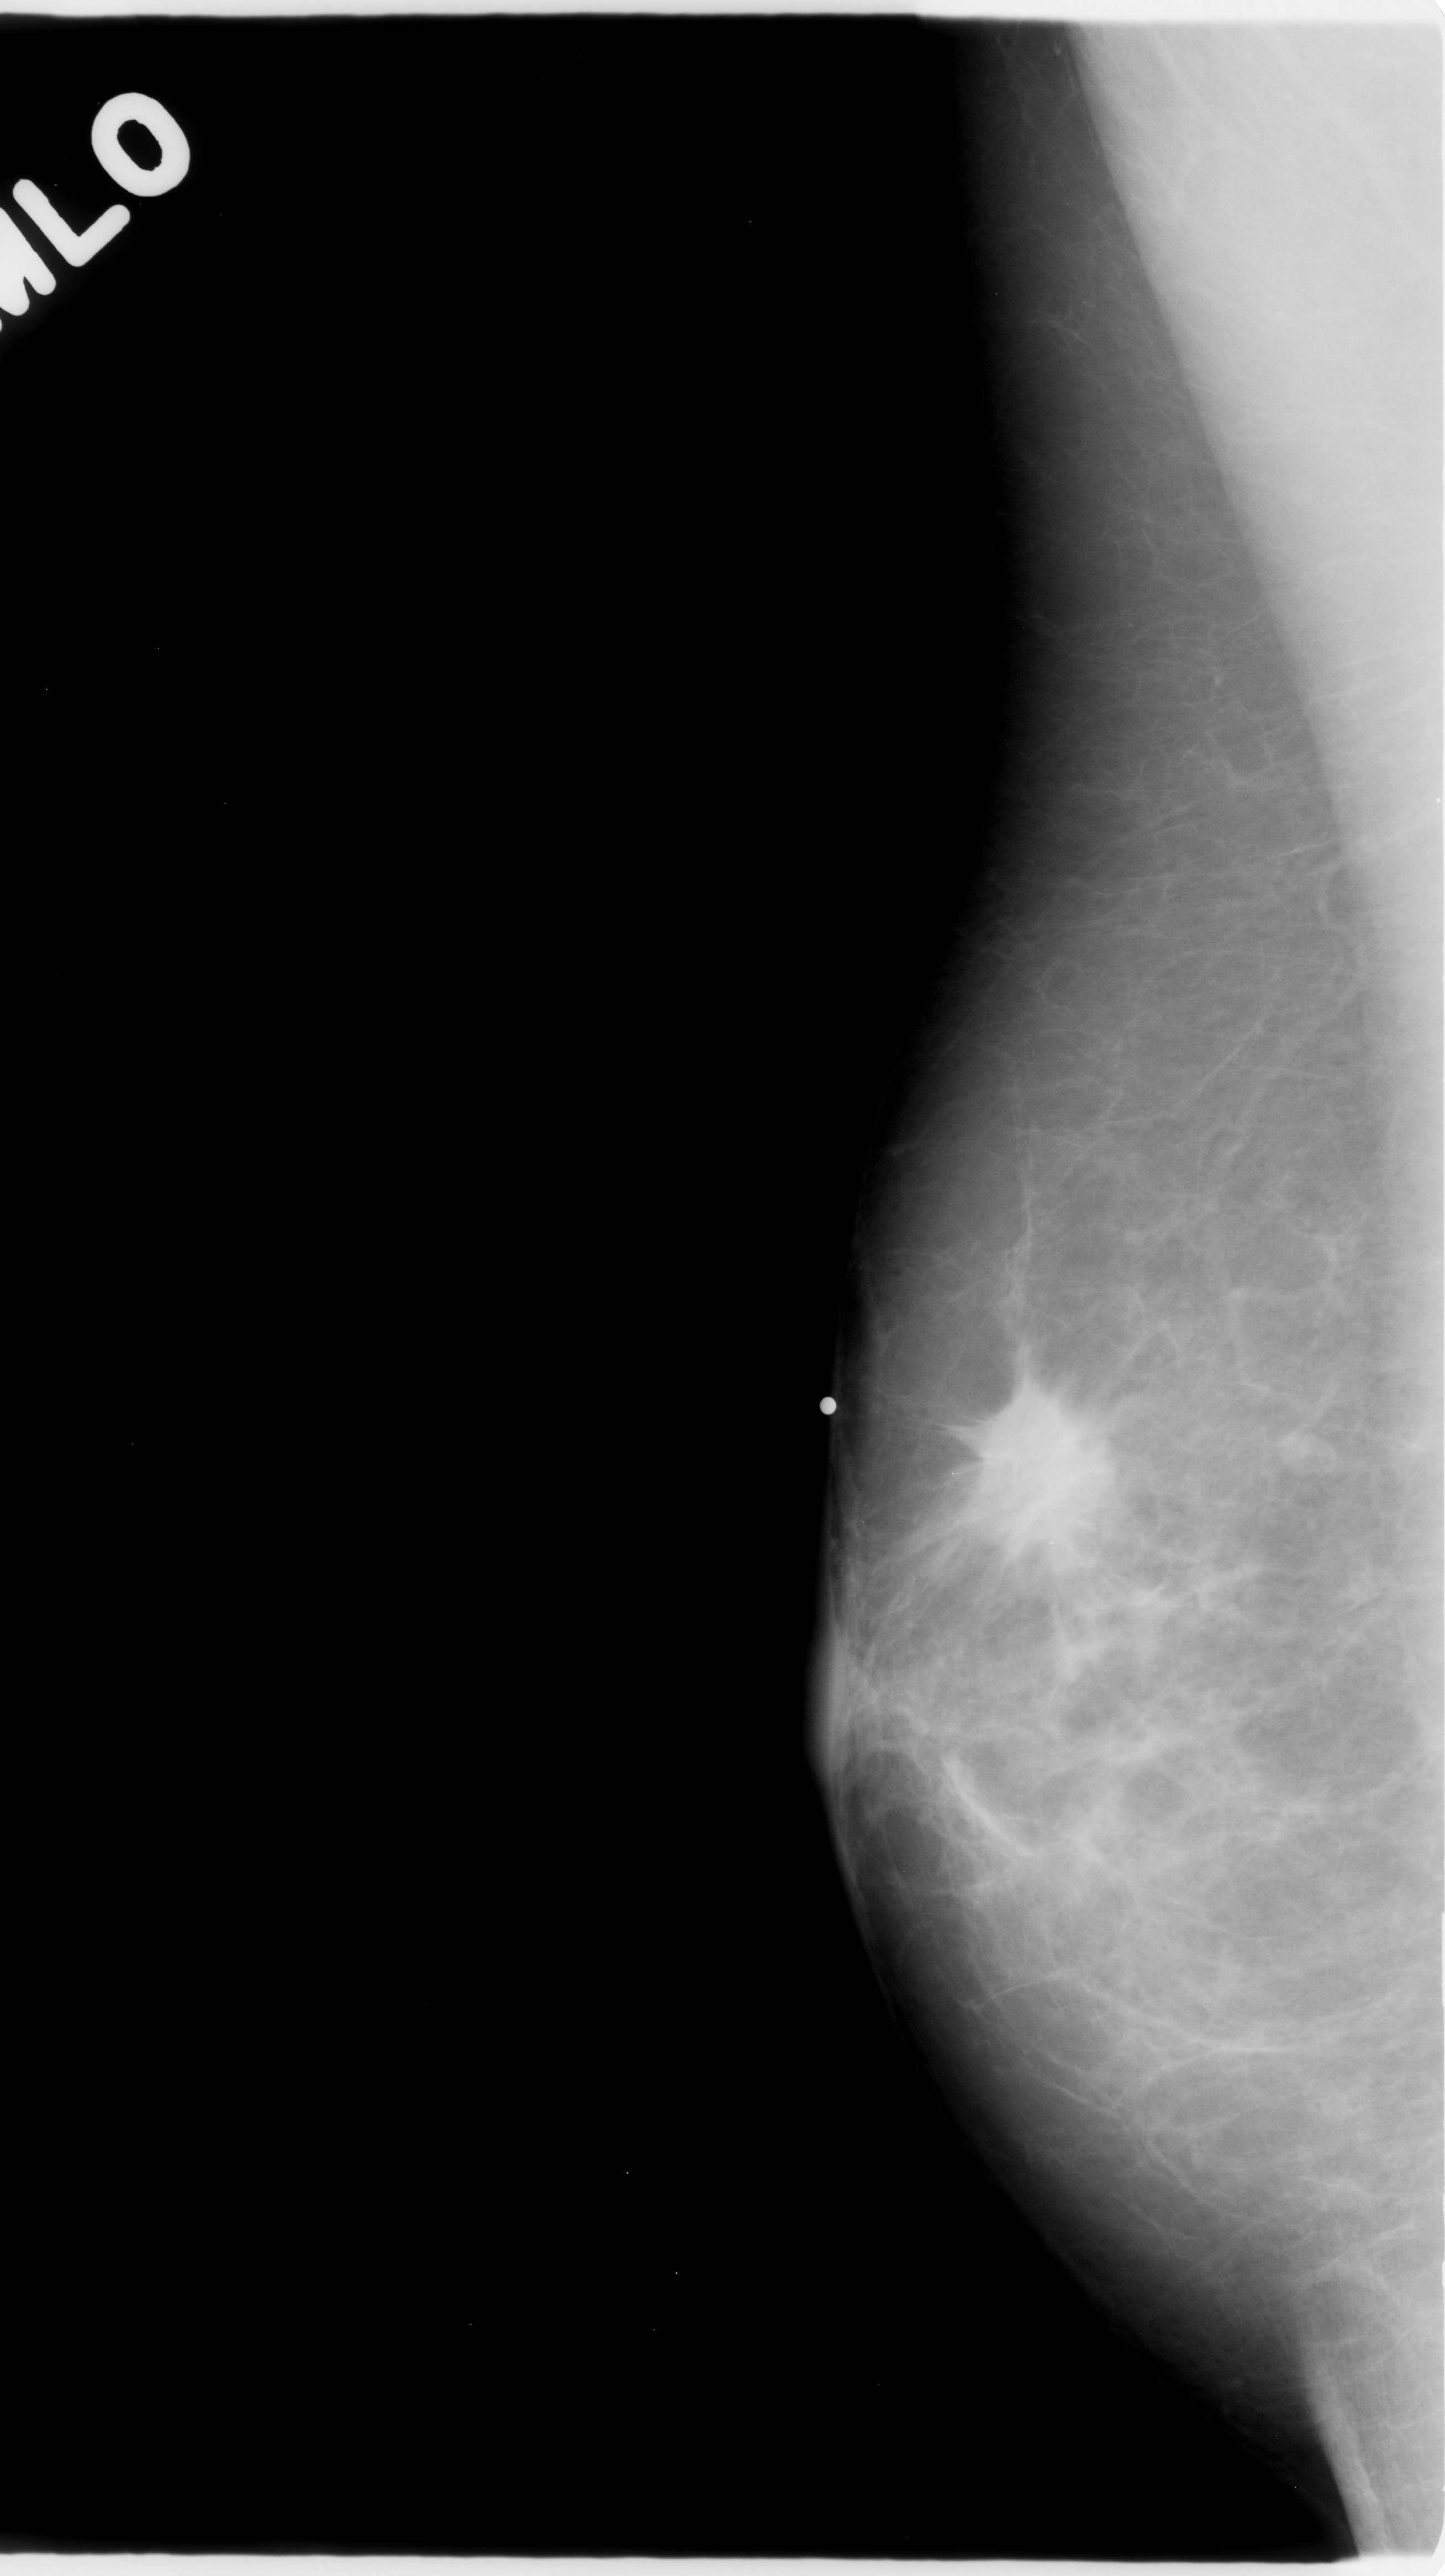
Digitized screen-film mammogram, right breast, mediolateral oblique (MLO) view, breast composition: almost entirely fatty (BI-RADS density category 1 of 4).
Marked findings (only marked abnormalities are described; nothing is implied about the rest of the image): mass, shape irregular, margins spiculated; BI-RADS assessment category 5; pathology (as recorded): malignant.